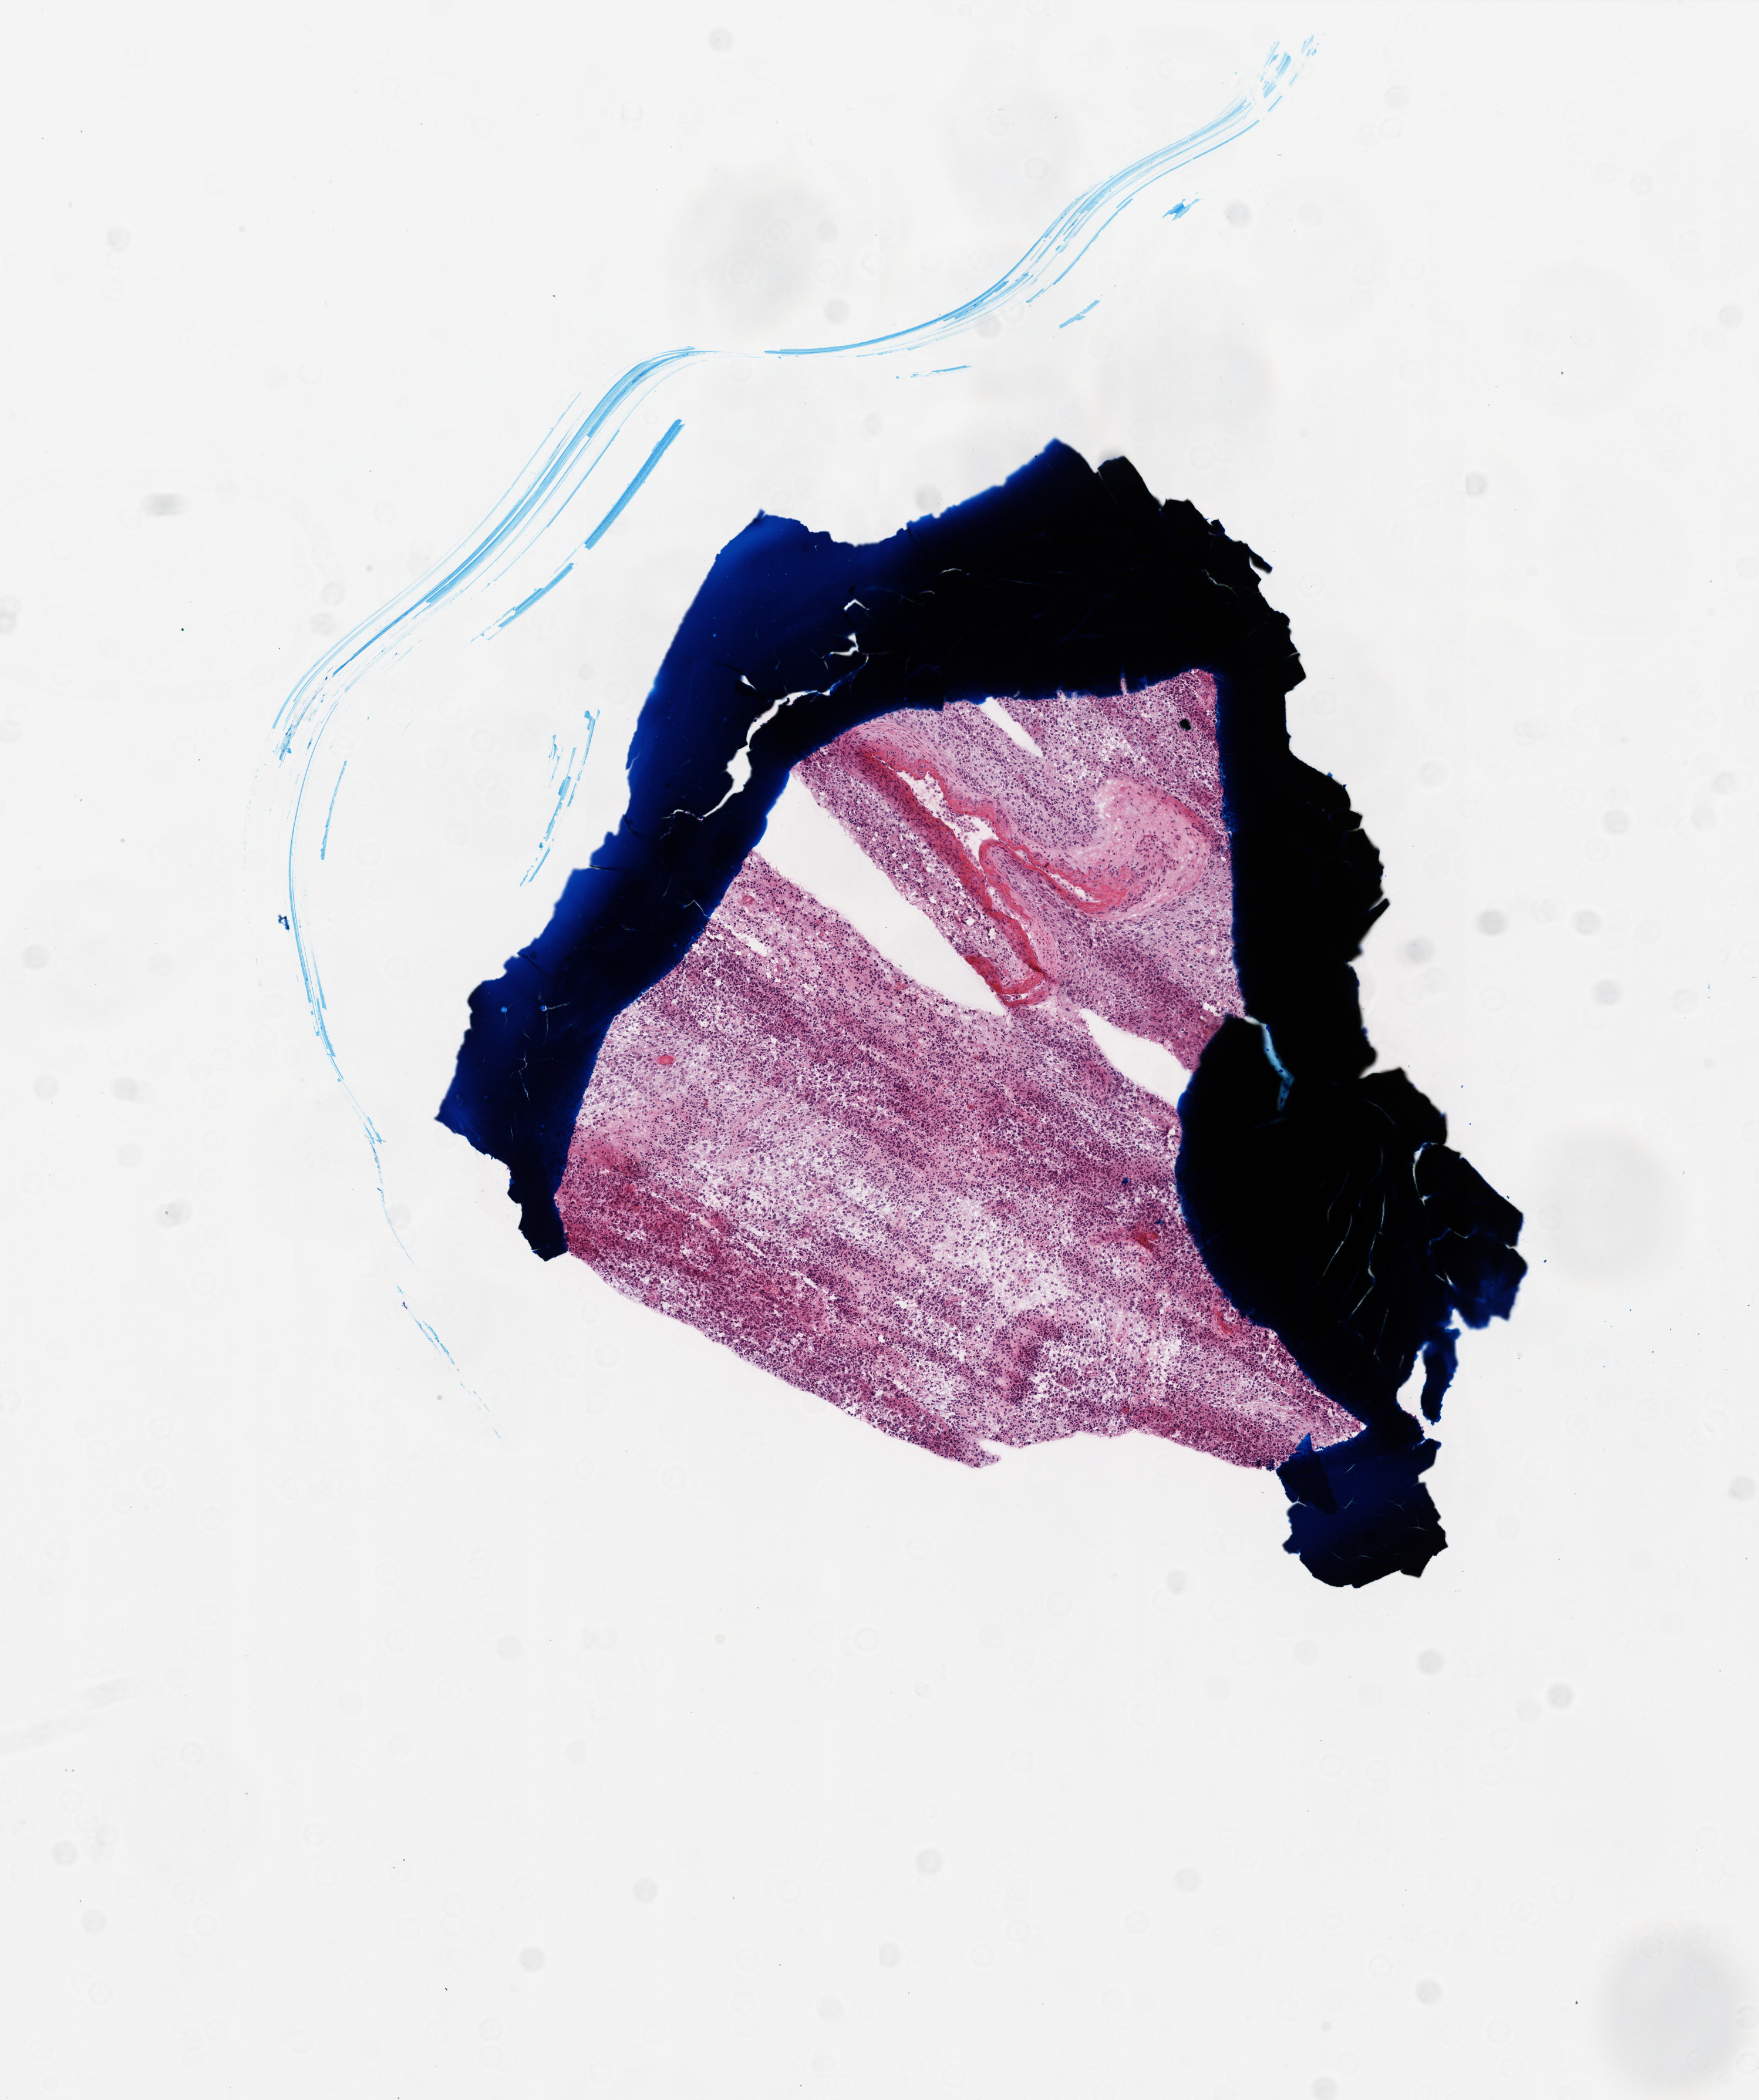
H&E whole-slide image — a low-resolution overview of the entire scanned area, about 6.0 x 7.2 mm (slide scanned at 20x), frozen section from the top of the tissue portion, sample: primary tumour, brain. Male, age 54 years at initial diagnosis. Composition of this section per pathologist review: tumour cells 90%, tumour nuclei 100%.
Pathologic diagnosis: Glioblastoma.